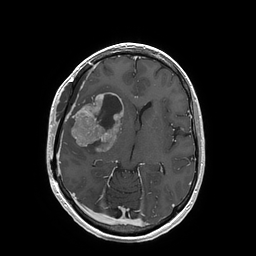
Brain MRI from a brain-tumour surgery series, one axial slice. Position 92 of 202 along the scan axis. T1-weighted post-contrast. 1 mm slice thickness. 256 × 256 image matrix, field of view 250 × 250 mm. From the clinical record (not read from this slice): histopathology: Glioblastoma; WHO grade: 4; IDH mutation: no.
Annotated regions visible in this slice (manually delineated by an expert):
- tumour: bounding box (x1, y1, x2, y2) in pixels: (71, 93, 123, 152)